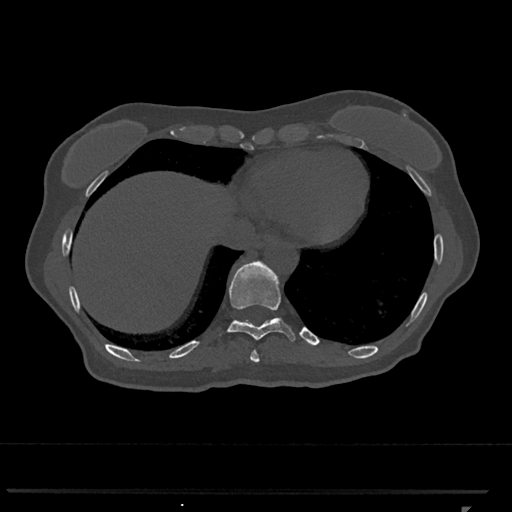
CT including the spine, one axial slice. Reconstruction kernel Br40s/3. Bone window (W 1800 / L 400 HU). 512 × 512 image matrix, field of view 380 × 380 mm. Patient: female, 62 years. Case-level facts recorded for this patient, not image findings: primary cancer: renal.
Annotated regions visible in this slice (semi-automatic segmentation, software-assisted and operator-edited):
- T10 vertebra: bounding box <227,261,296,341> (left, top, right, bottom; pixels)
- T9 vertebra: <250,350,260,362>